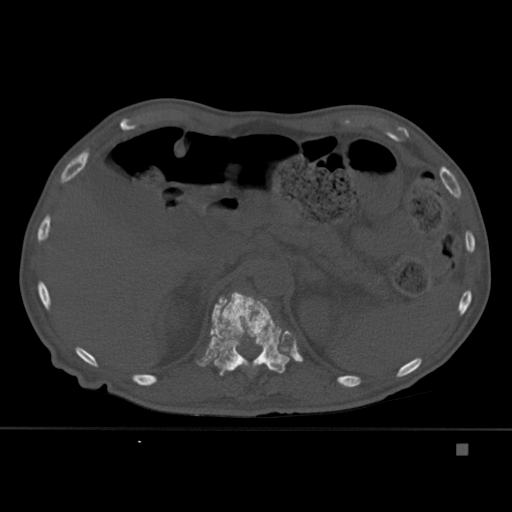
CT including the spine, one axial slice. Slice 202 of 451 in the series (ordered by position). Bone window (W 1800 / L 400 HU). 1.5 mm slice thickness. 512 × 512 image matrix, field of view 378 × 378 mm. Male patient, age 75 years. From the clinical record (not read from this slice): primary cancer: prostate.
Outlined on this slice (semi-automatically segmented with operator editing):
- T11 vertebra: bounding box [x1, y1, x2, y2] px = [257, 363, 267, 366]
- T12 vertebra: [210, 292, 290, 376]